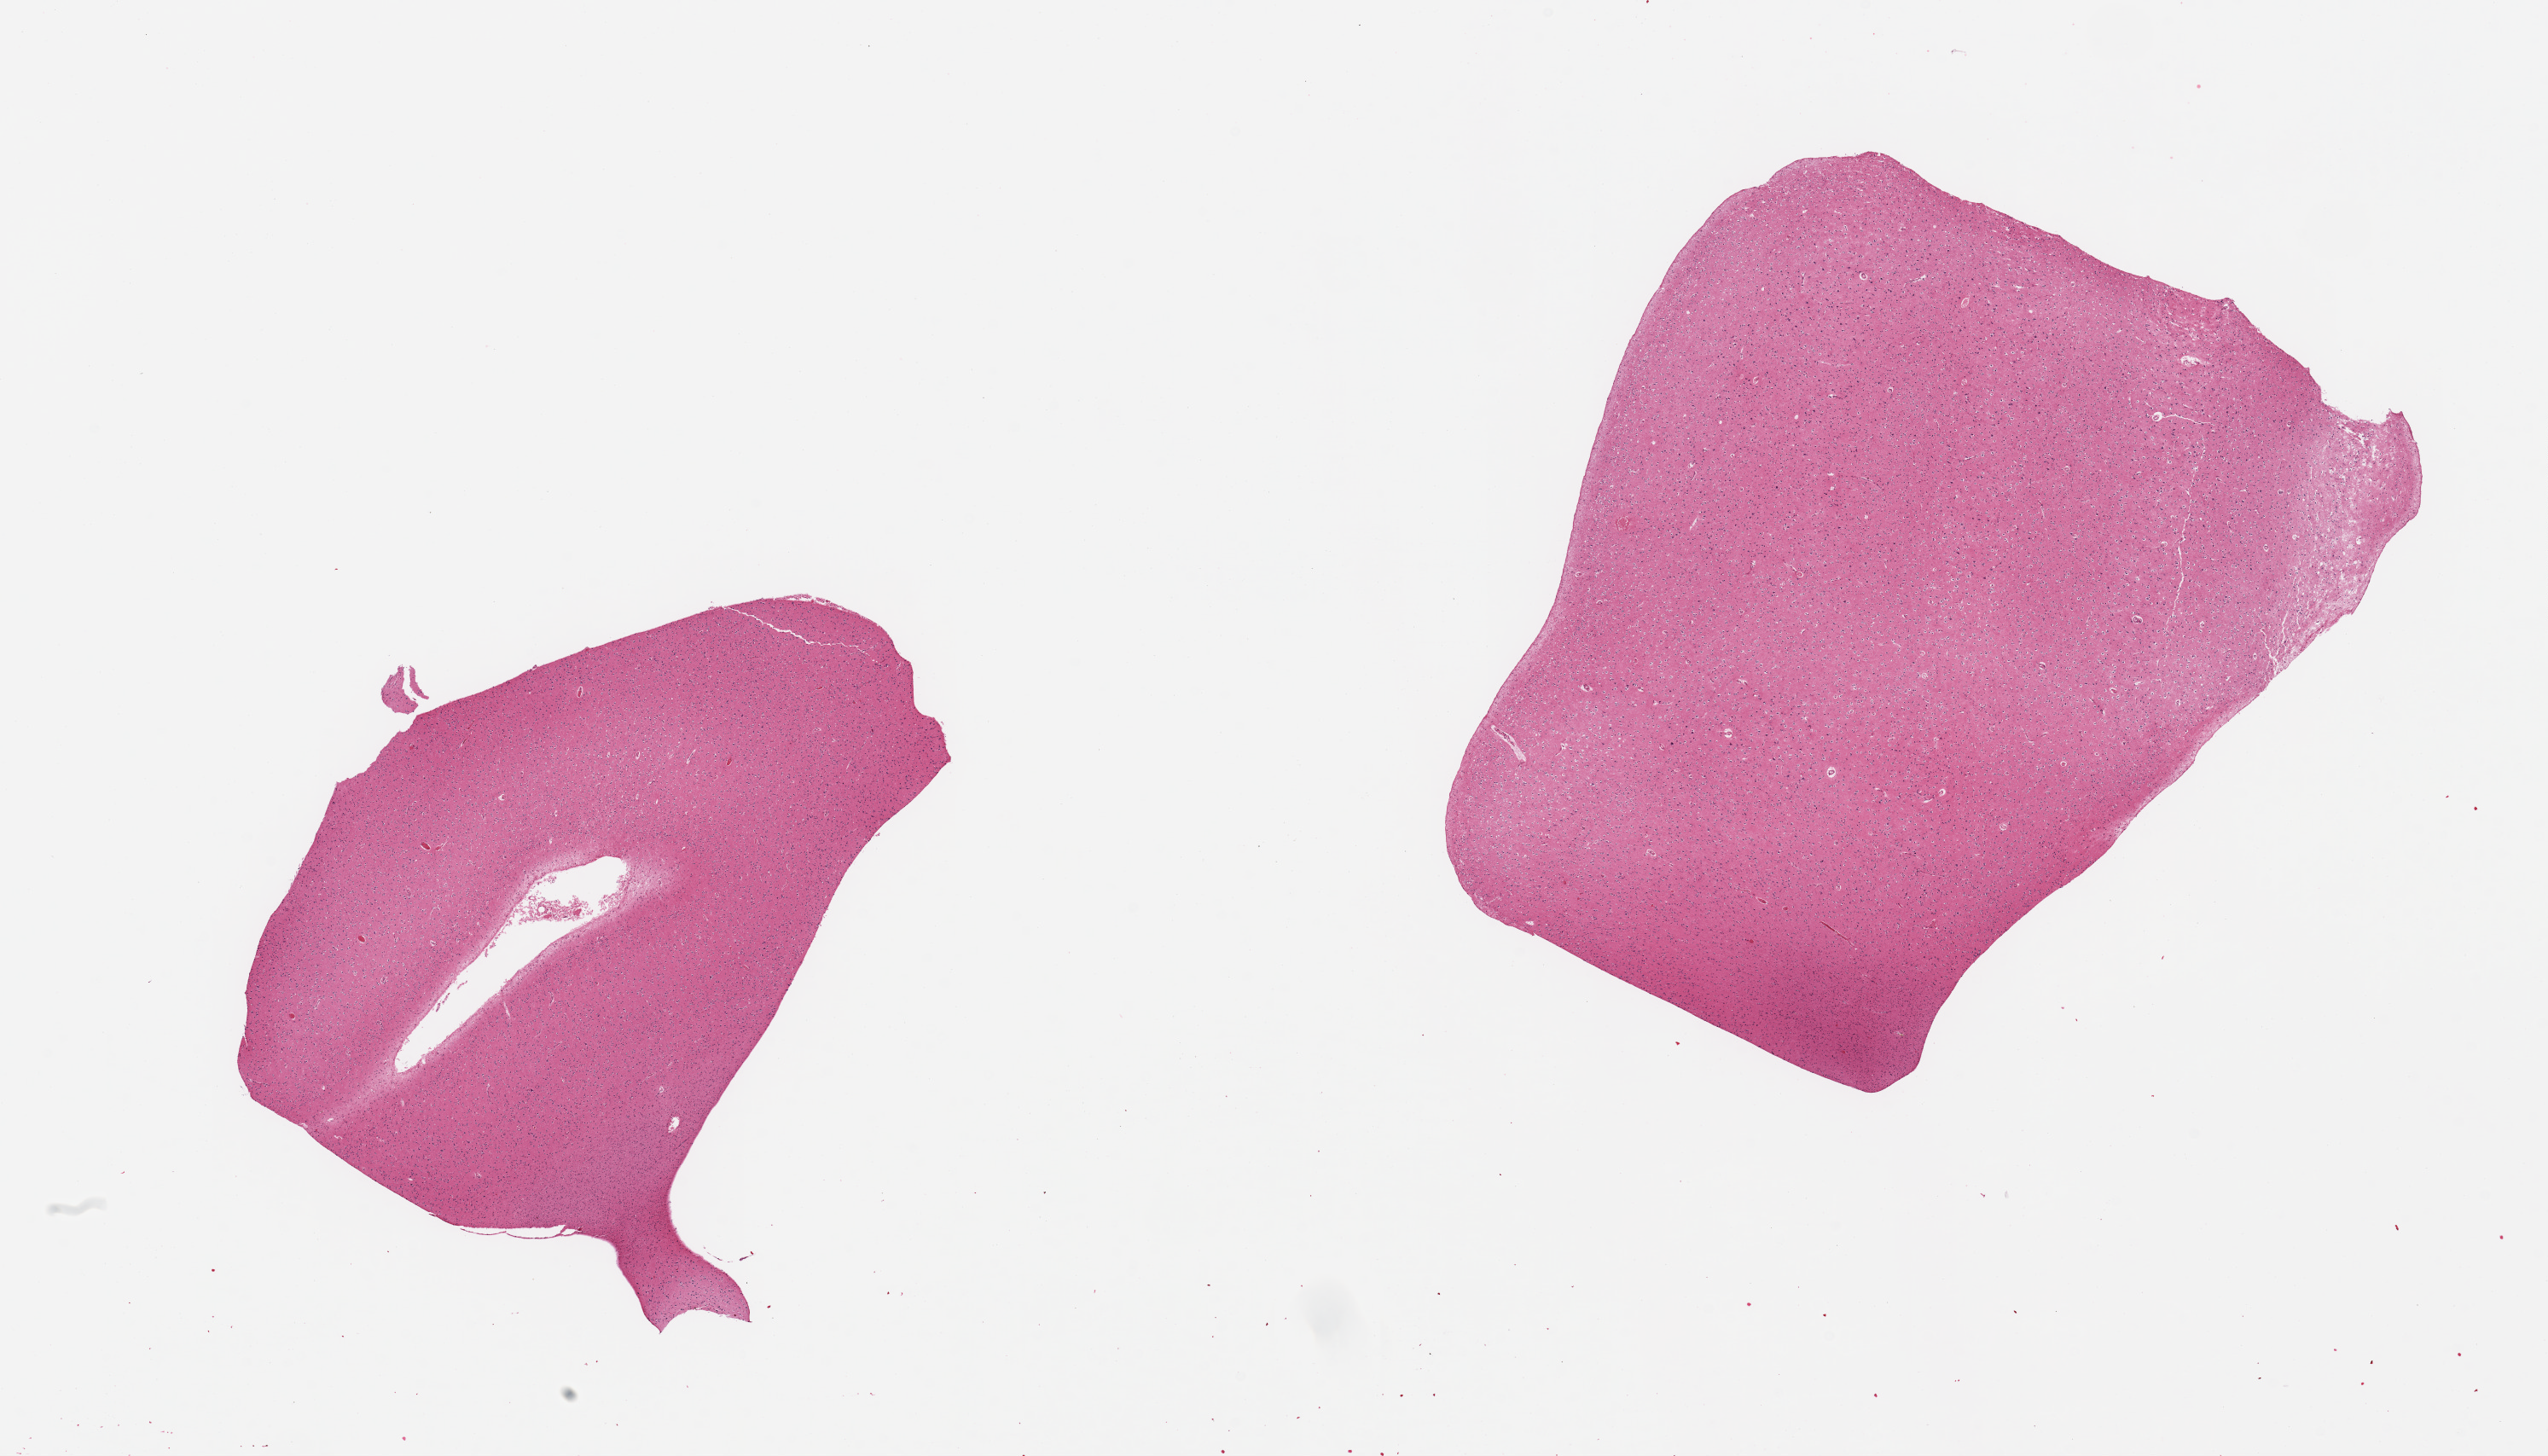
Whole-slide image, hematoxylin and eosin (H&E) stain, a low-resolution overview of the entire scanned area, about 23.6 x 13.5 mm (slide scanned at 20x). PAXgene-fixed, paraffin-embedded tissue. Sampled site (target tissue): cerebral cortex. Donor tissue sample. Donor sex: male.
Pathologist's review note for this sample: 2 pieces.